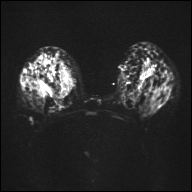
Breast MRI, one axial slice; slice 22 of 32 in the series (ordered by position); diffusion-weighted series; image 2 of 4 stored at this slice position (different b-values; order by instance number); 1.5 T; 4 mm slice thickness; 192 × 192 image matrix, field of view 360 × 360 mm. Female patient.
Structures marked on this image (expert manual segmentation):
- tumour on diffusion-weighted imaging: bounding box <43,63,61,97> (left, top, right, bottom; pixels)